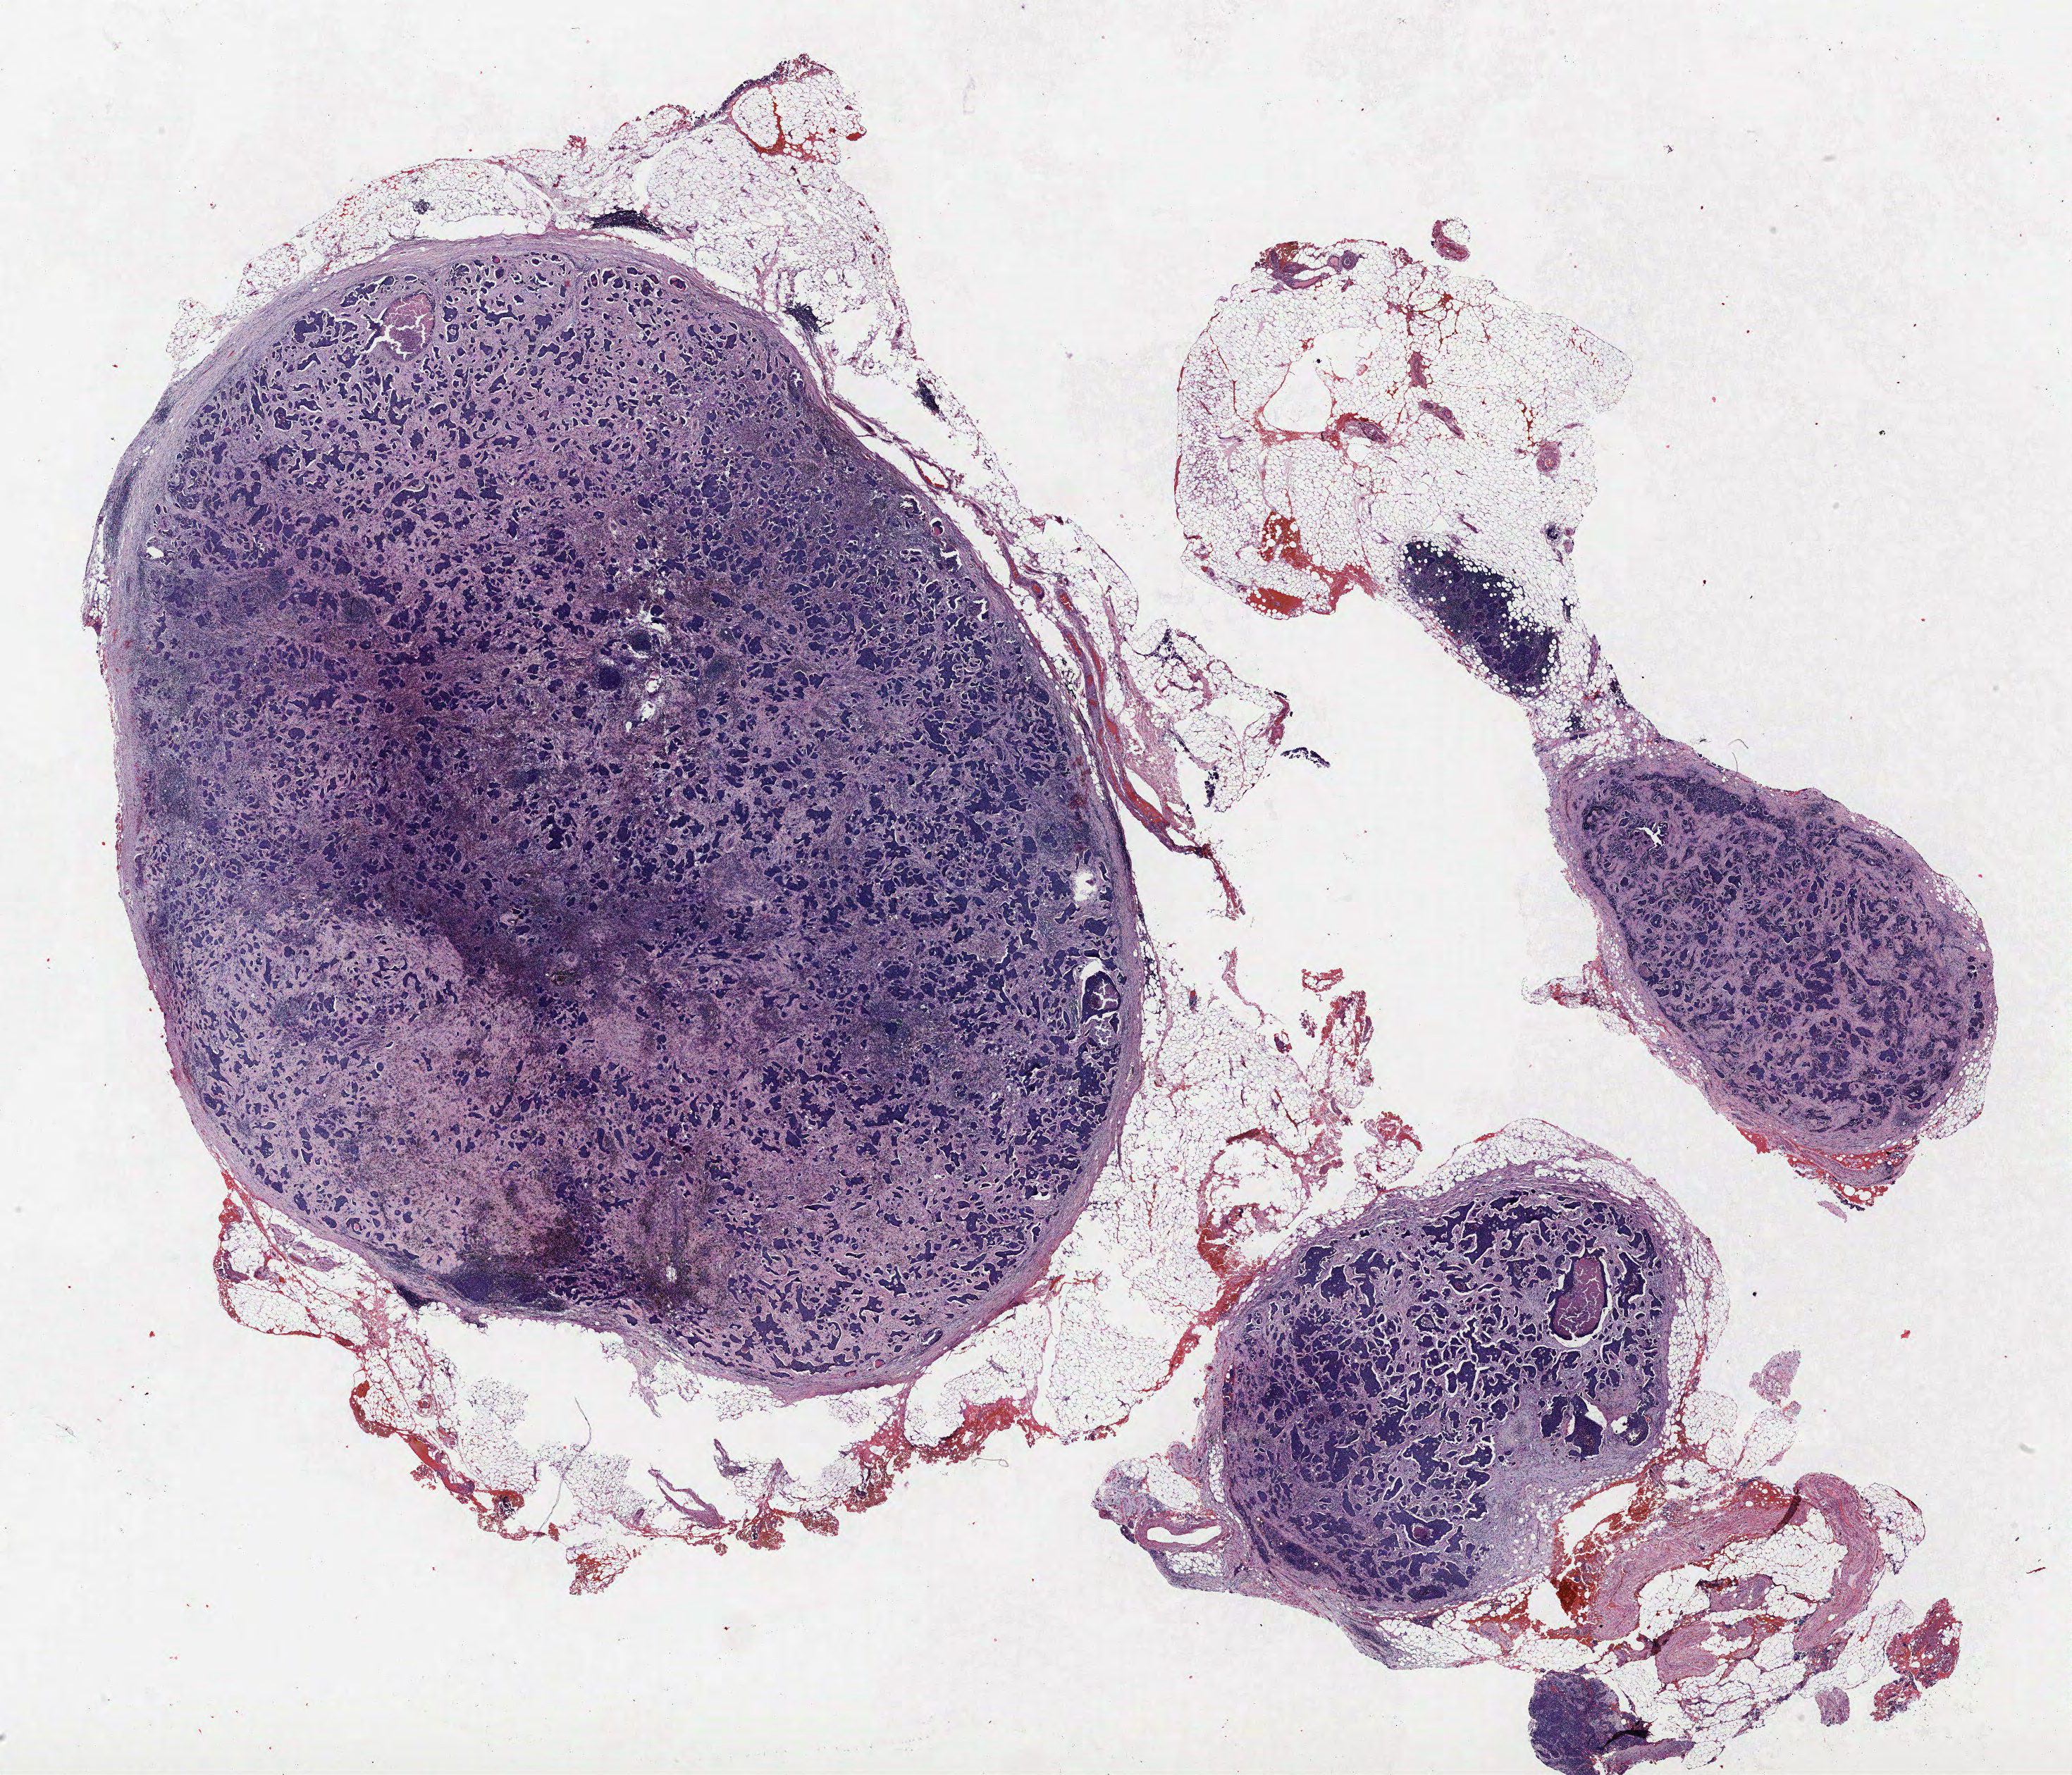
Whole-slide histology image, H&E-stained, shown as a low-resolution overview of the whole scanned area (about 23.5 x 20.2 mm, acquisition: 40x scan); FFPE section; lung. Male, age 68 at enrolment. Grade: poorly differentiated (G3).
• primary tumour location (clinical record): right lower lobe
• tumour size (pathology): 30 mm
• stage (AJCC 6th edition): IIIA
• participant's lung-cancer diagnosis: Adenosquamous carcinoma
• ICD-O-3 topography: lower lobe of lung (C34.3)